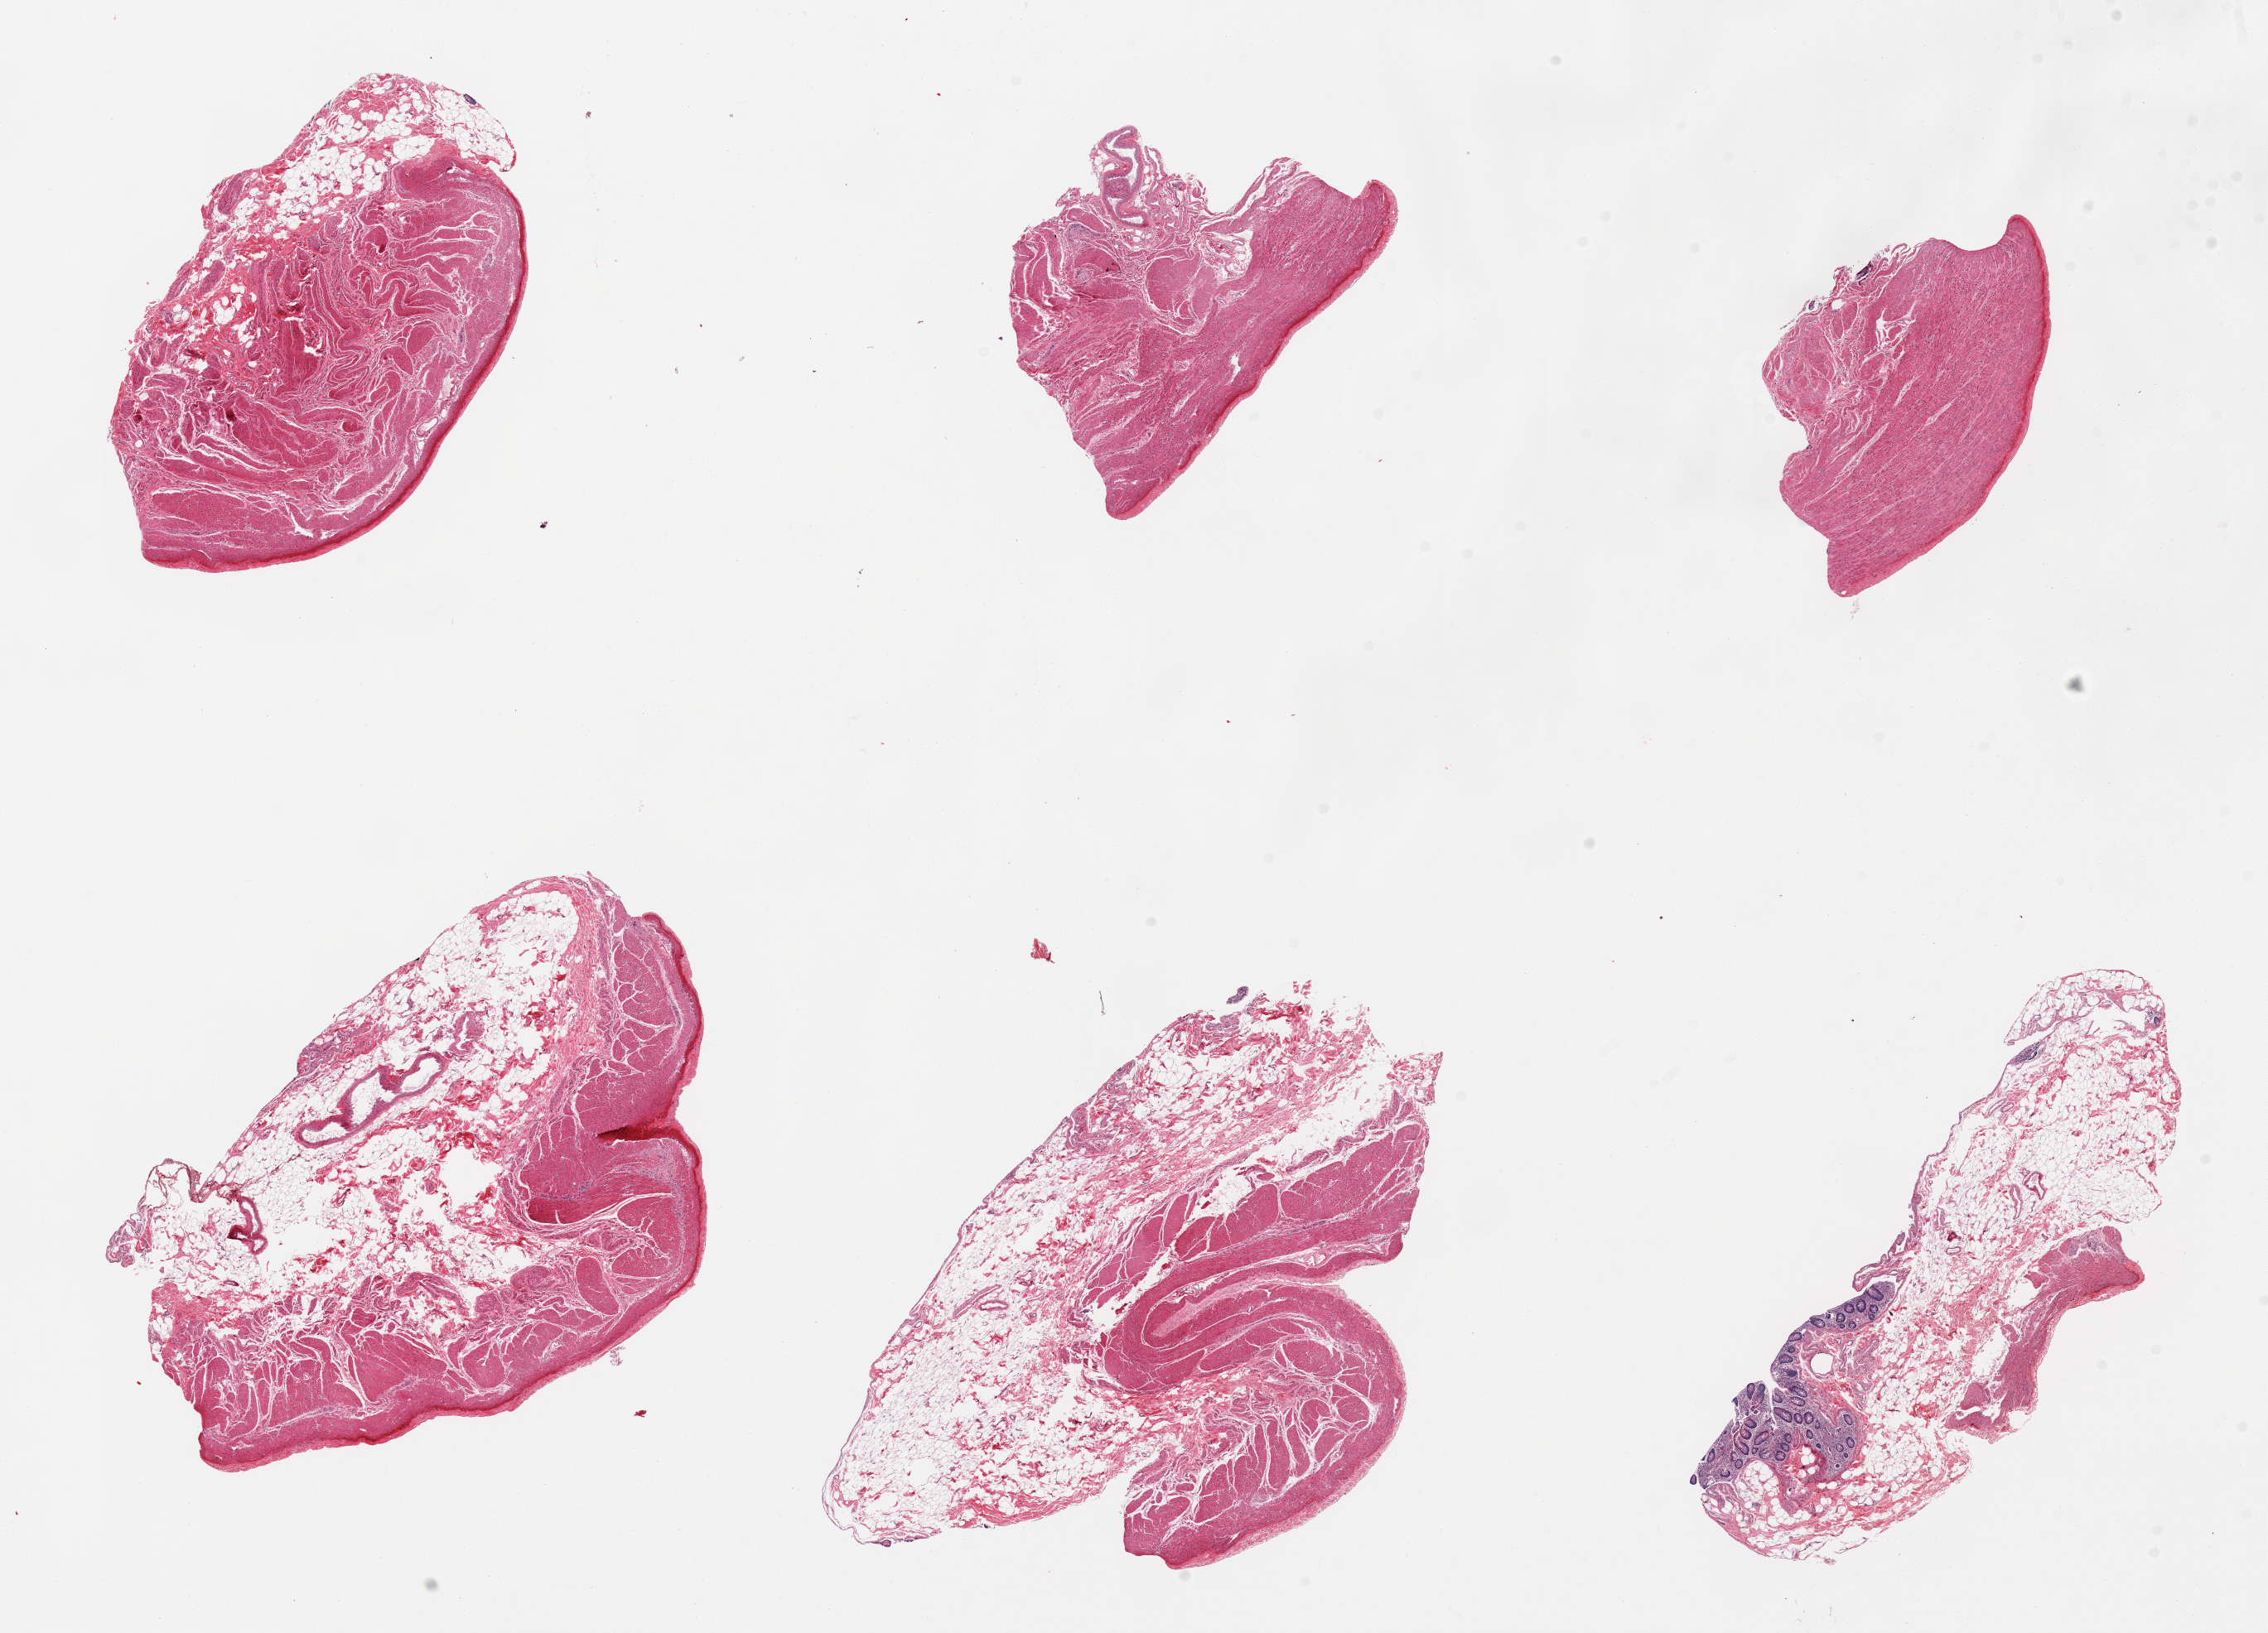
Whole-slide image, haematoxylin and eosin stain — whole scanned area (about 21.7 x 15.6 mm) shown as a low-resolution overview. PAXgene-fixed, paraffin-embedded tissue. Target tissue: sigmoid colon. Donor tissue sample.
Review note (as recorded): 6 pieces, target muscularis; one section is largely fat, autolyzed mucosa.